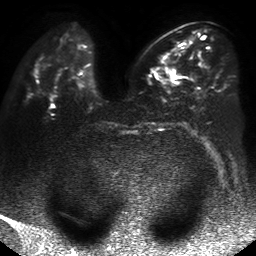
Breast MRI, one axial slice. Position 22 of 50 along the scan axis. Diffusion-weighted series; image 2 of 4 stored at this slice position (different b-values; order by instance number). 1.5 T. 4 mm slice thickness. 256 × 256 image matrix, field of view 360 × 360 mm. Female patient.
Outlined on this slice (expert manual segmentation):
- tumour on diffusion-weighted imaging: bounding box (x1, y1, x2, y2) in pixels: (168, 68, 175, 78)